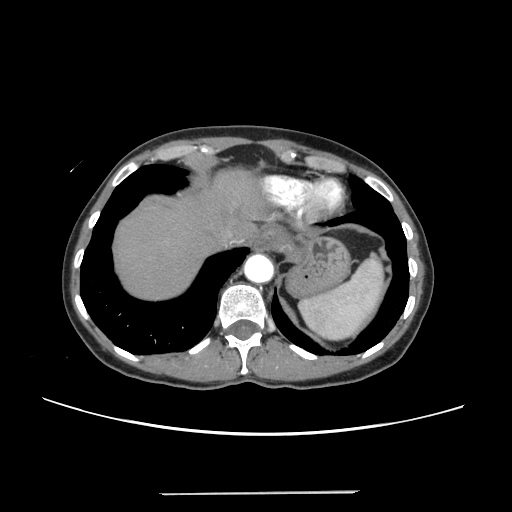
Contrast-enhanced abdominal CT, one axial slice; position 212 of 240 along the scan axis; intravenous contrast given; soft-tissue window (W 400 / L 40 HU); 512 × 512 image matrix, field of view 371 × 371 mm. Female patient, age 60 years. From the clinical record (not read from this slice): diagnosis: colorectal cancer liver metastases, imaged before liver resection; multiple liver metastases: no.
Annotated regions visible in this slice (manually delineated by an expert):
- hepatic veins: bounding box [x1, y1, x2, y2] px = [223, 231, 232, 240]
- liver: [114, 172, 261, 300]
- planned liver remnant (the part of the liver to remain after resection): [114, 171, 261, 300]